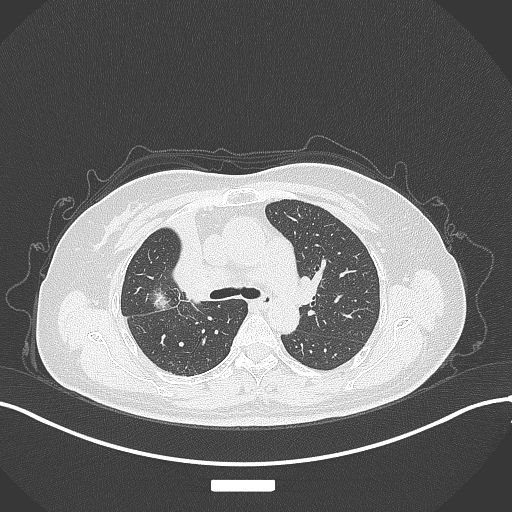
Chest CT, one axial slice. Slice 205 of 309 in the series (ordered by position). Lung window (W 1500 / L -600 HU). 1 mm slice thickness. 512 × 512 image matrix. Female patient, age 60 years. From the clinical record (not read from this slice): clinical TNM (as recorded): T3 N1 M1.
Annotated regions visible in this slice (bounding box drawn by a radiologist):
- lung tumour (recorded histology: adenocarcinoma): bounding box [x1, y1, x2, y2] px = [146, 286, 184, 319]